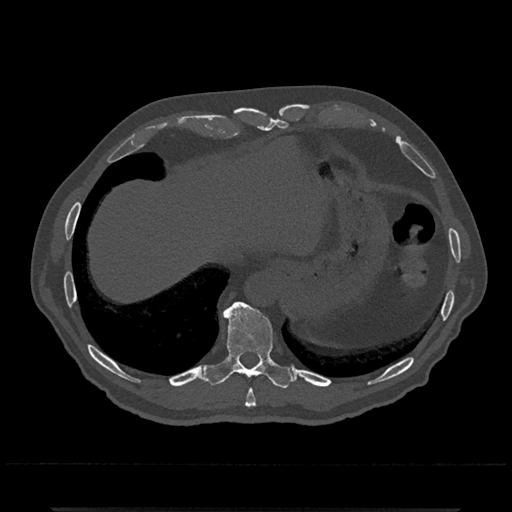
CT including the spine, one axial slice; reconstruction kernel Br40s/3; 120 kVp; bone window (W 1800 / L 400 HU); 0.5 mm slice thickness; 512 × 512 image matrix. Male patient, age 67 years. Case-level facts recorded for this patient, not image findings: primary cancer: prostate.
Annotated regions visible in this slice (semi-automatically segmented with operator editing):
- T10 vertebra: bounding box <203,301,293,389> (left, top, right, bottom; pixels)
- T9 vertebra: <245,389,256,407>